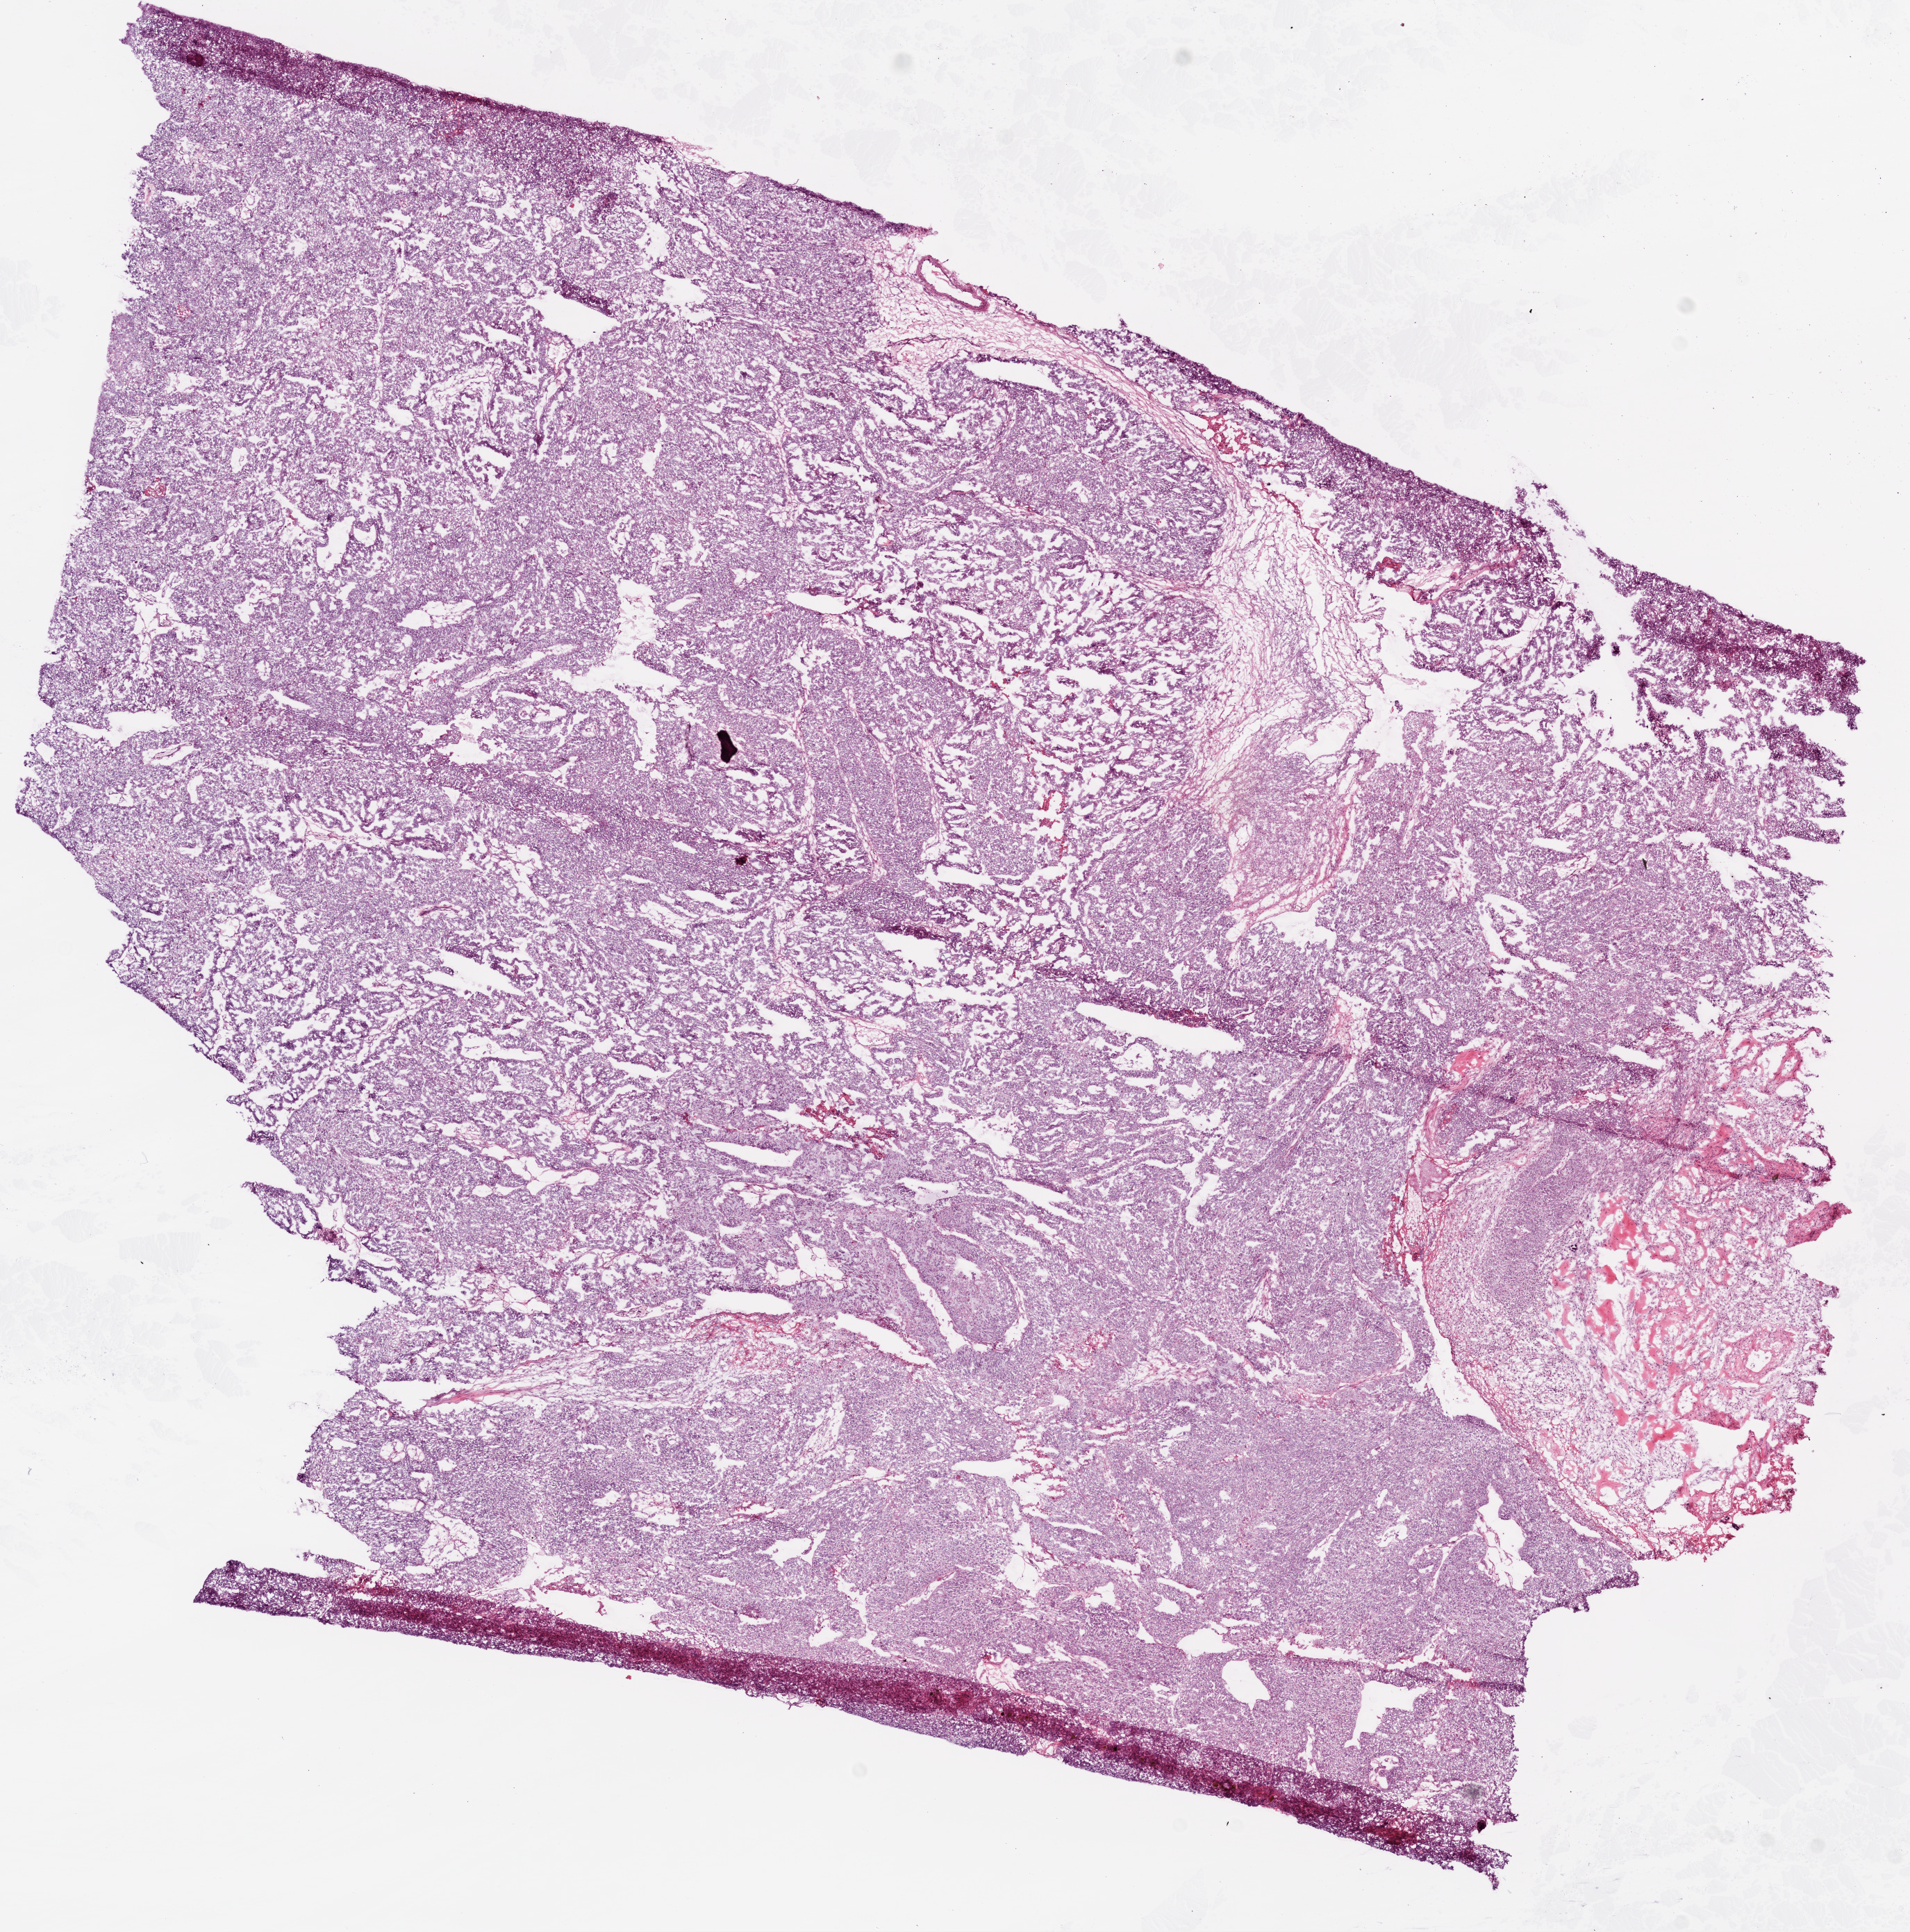
H&E whole-slide image — shown as a low-resolution overview of the whole scanned area (about 11.0 x 11.2 mm, from a 20x scan); frozen section; ovary, primary tumour sample. Female, age 53 years at initial diagnosis. Histologic grade: G3 (poorly differentiated). Composition of this section per pathologist review: tumour cells 80%, tumour nuclei 95%, normal cells 8%, stromal cells 0%, necrosis 12%.
FIGO stage: IIIB. Histologic diagnosis: Serous cystadenocarcinoma, NOS.